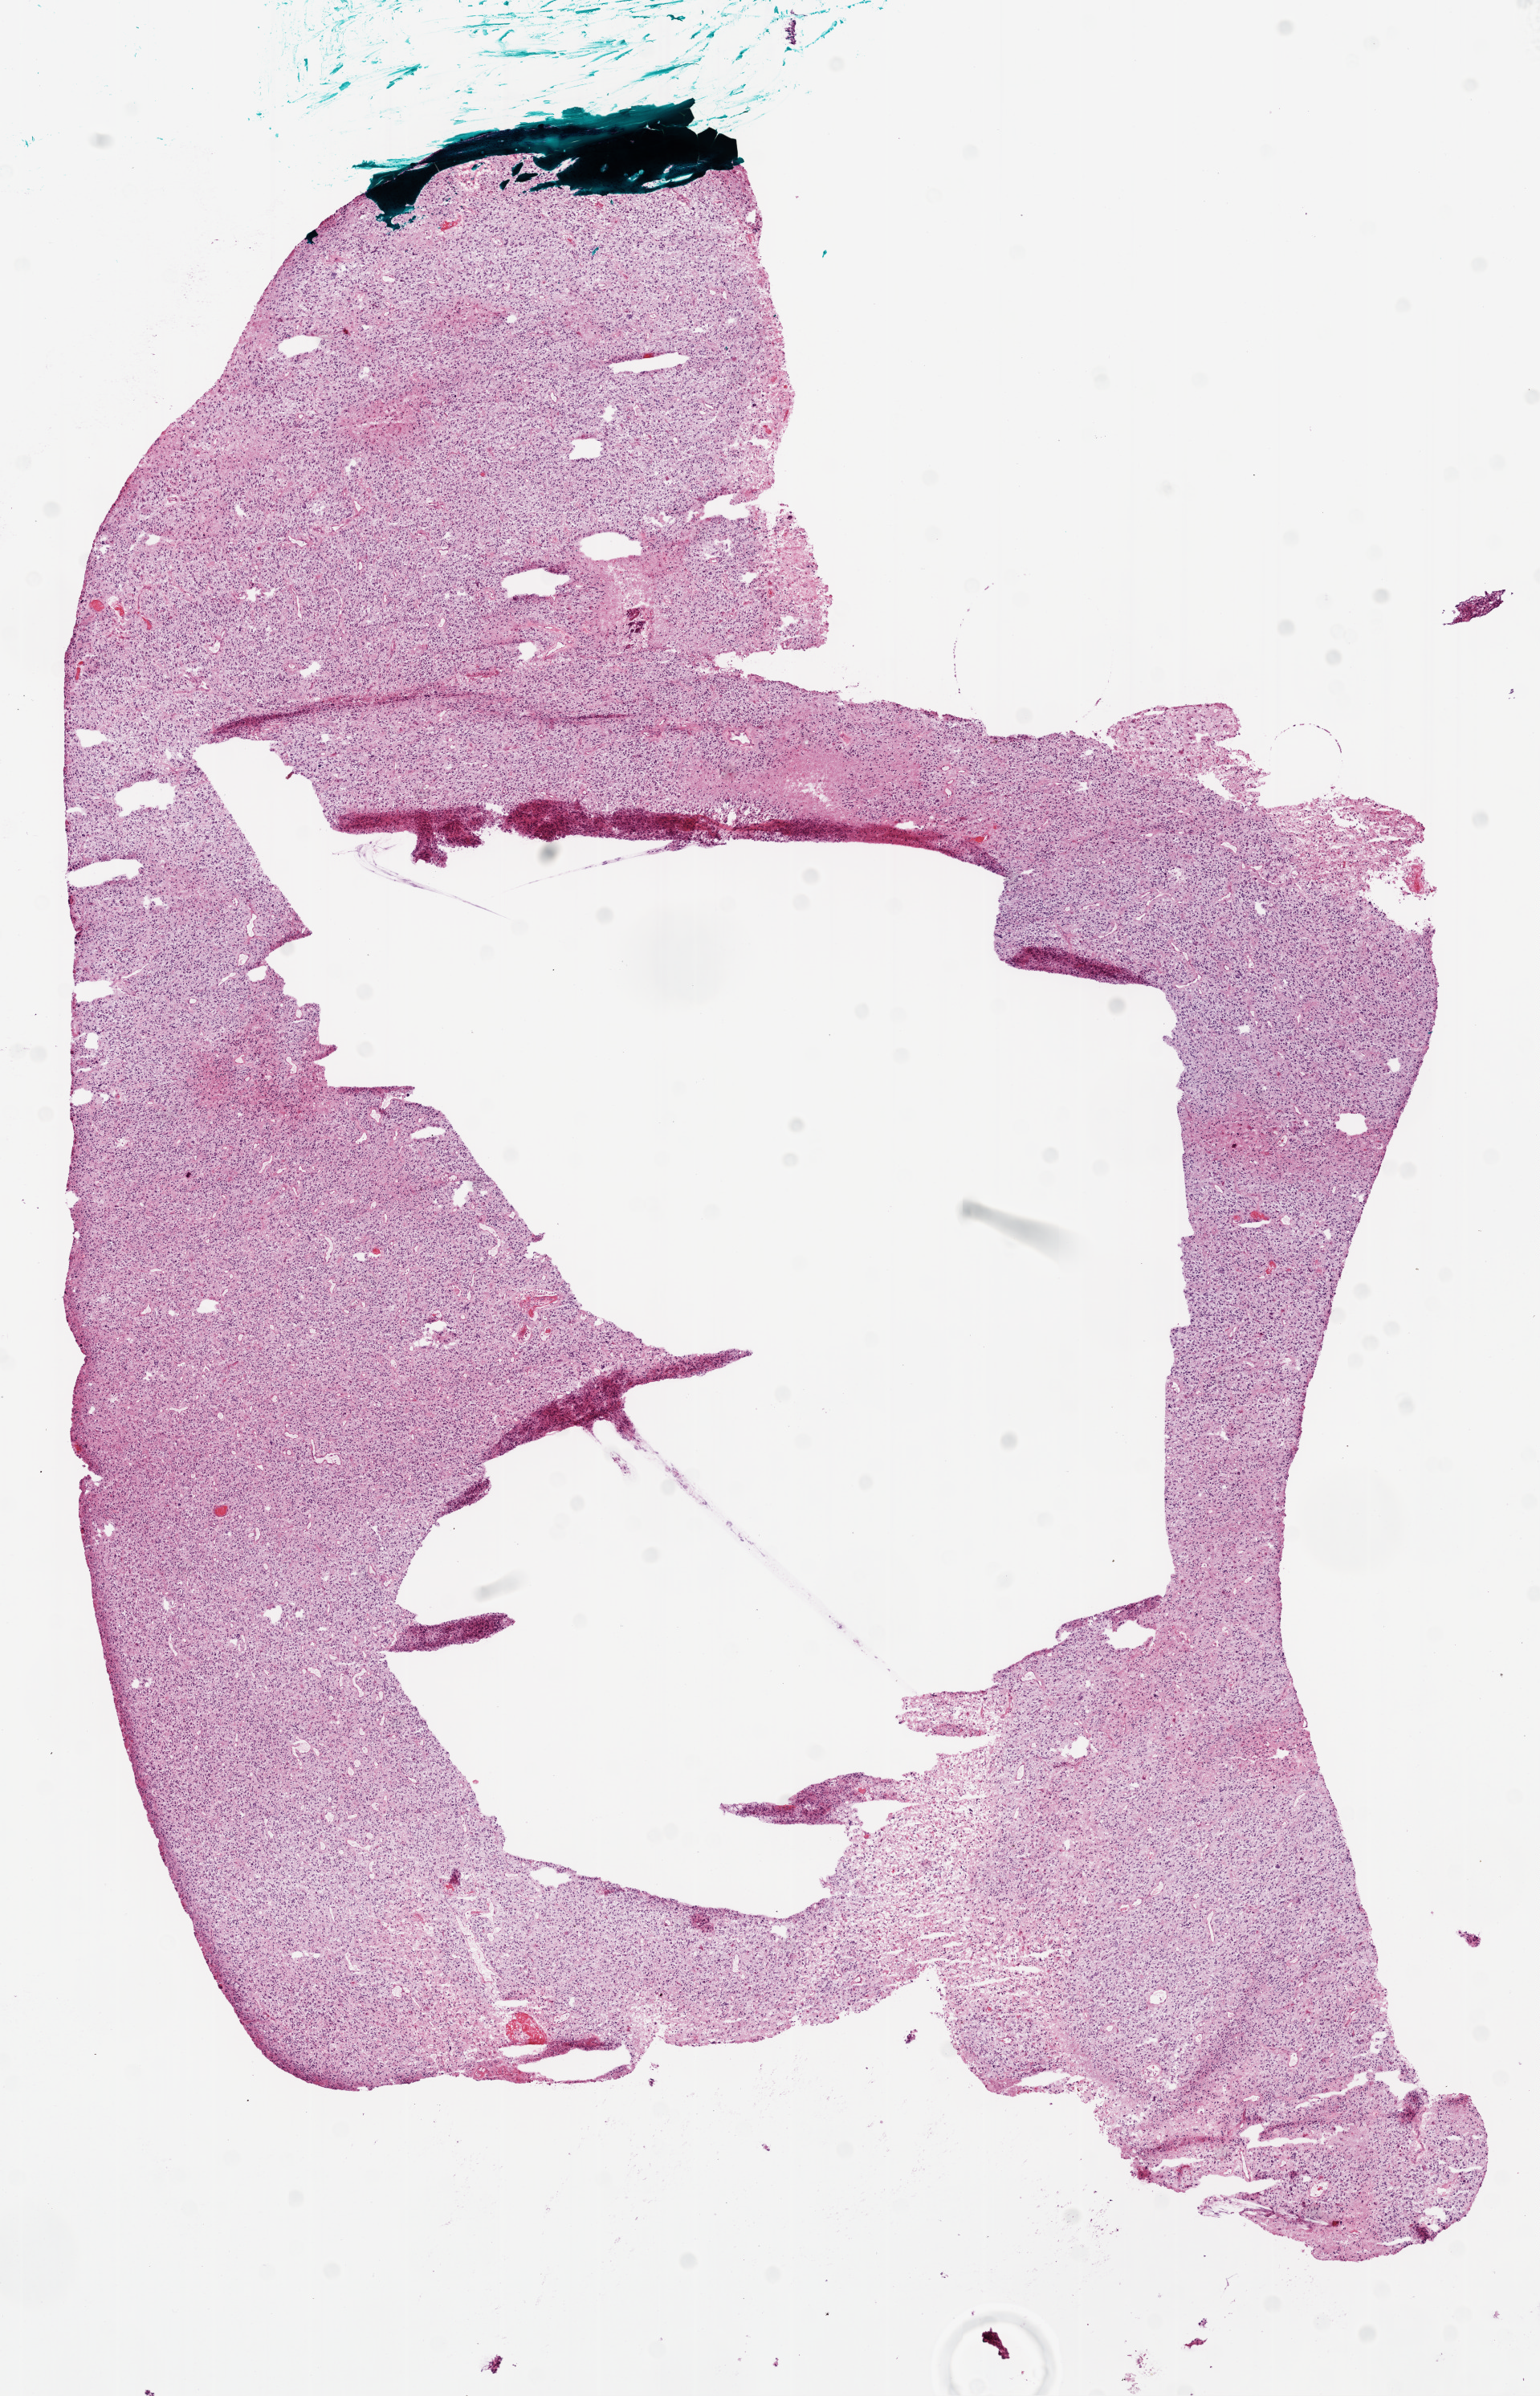
H&E-stained whole-slide image, whole scanned area (about 7.7 x 12.0 mm) shown as a low-resolution overview; frozen section; primary tumour sample from the brain. Male, age 49 years at initial diagnosis. Composition of this section per pathologist review: tumour cells 90%, tumour nuclei 100%.
Histologic diagnosis: Glioblastoma.